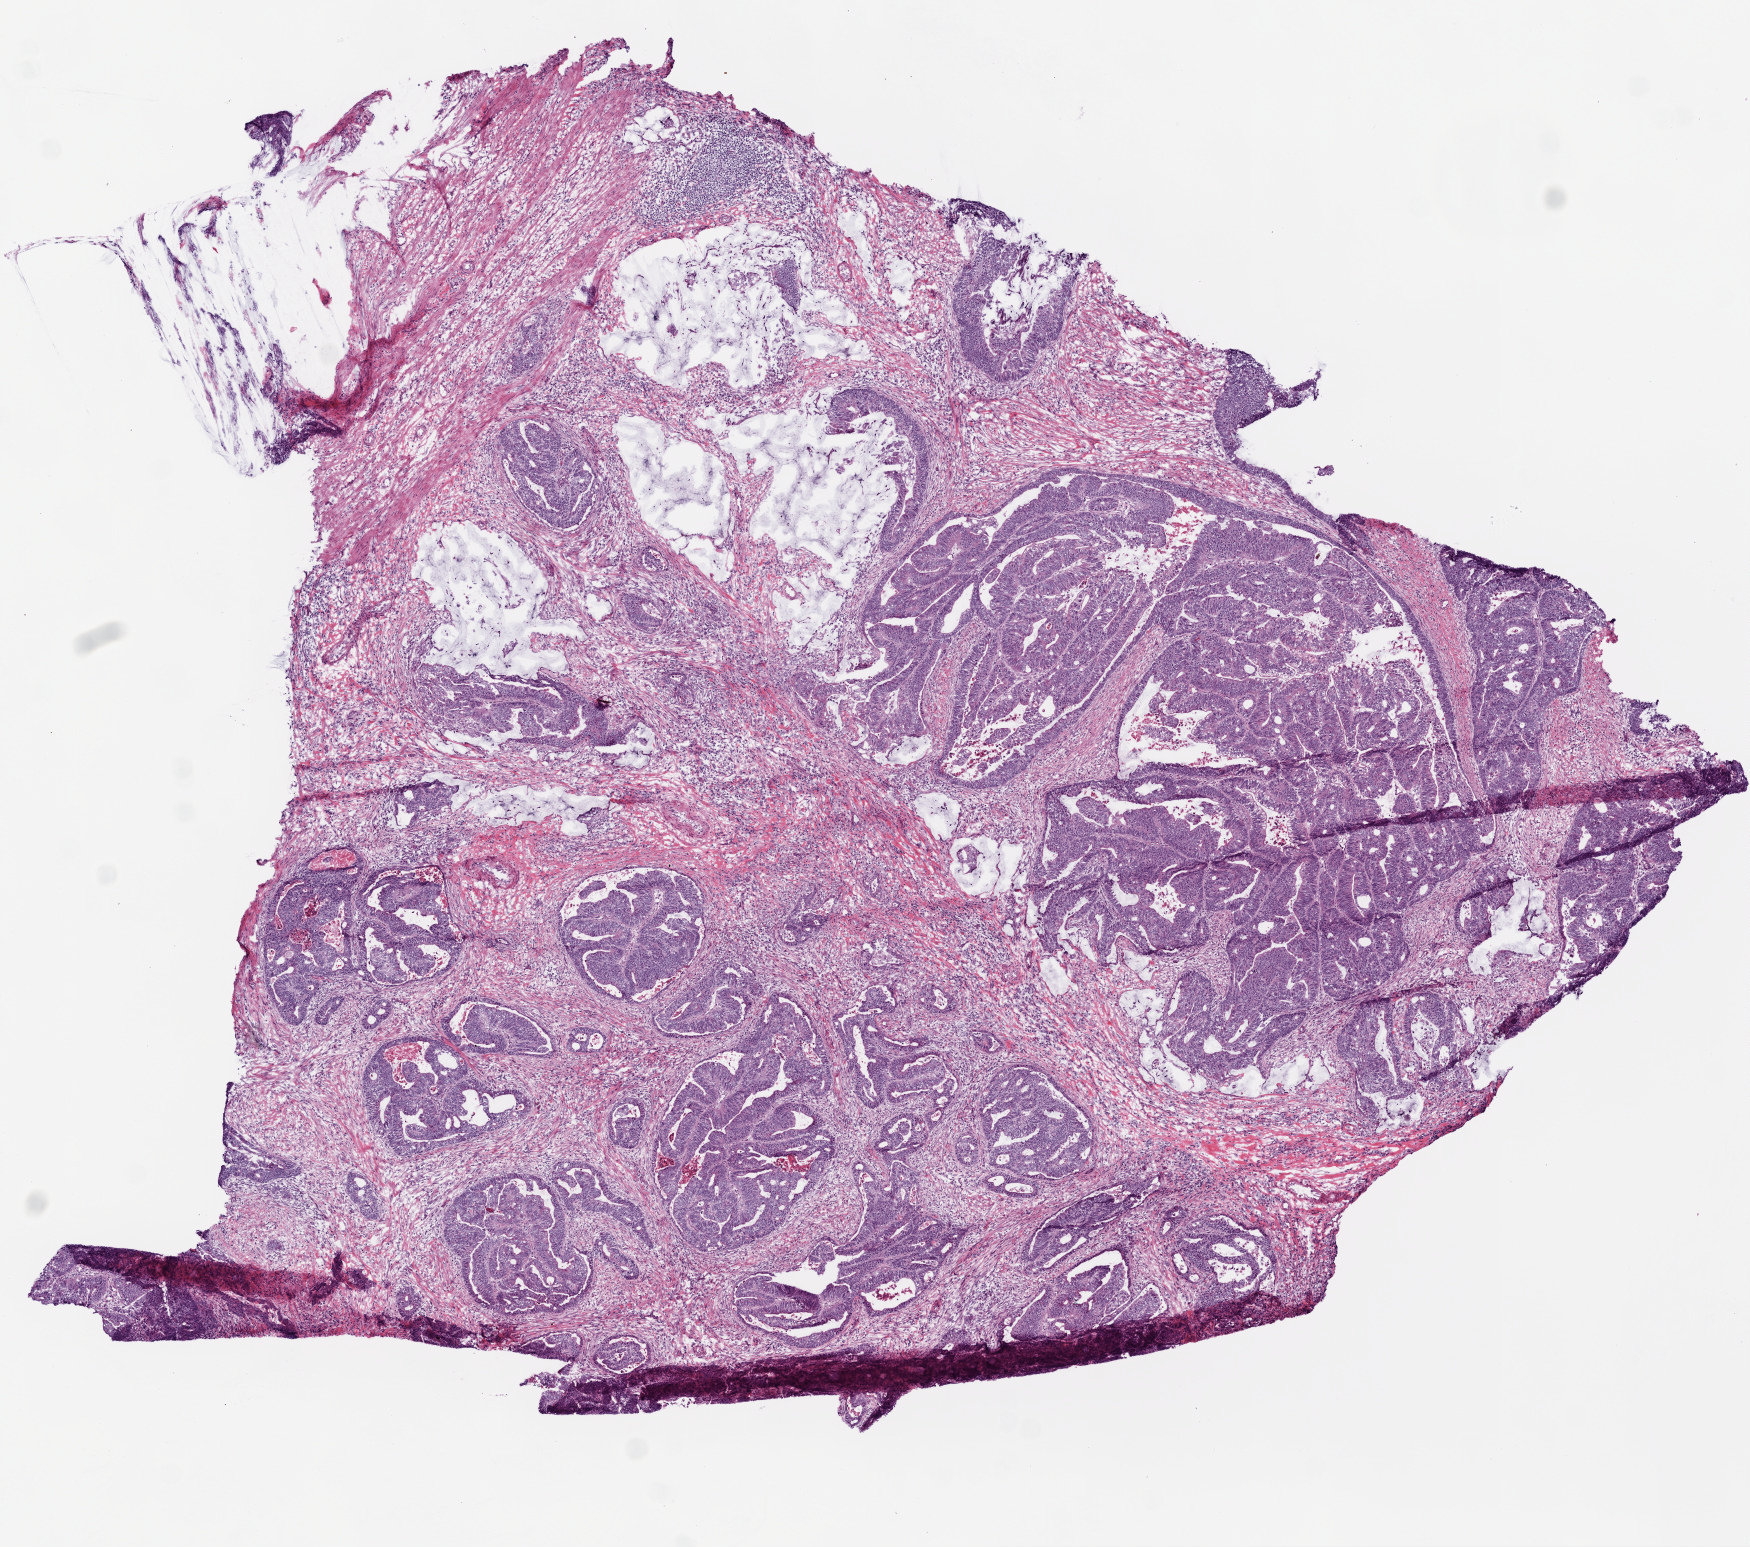
Digitized H&E-stained tissue section (whole slide) — a low-resolution overview of the entire scanned area, about 7.0 x 6.2 mm, frozen section, primary tumour sample from the colon. Female patient; age at initial diagnosis 53 years. Pathologist review of this section (percent, as recorded): tumour cells 25%, tumour nuclei 60%, normal cells 0%, stromal cells 70%, necrosis 5%.
* AJCC pathologic stage: II (5th edition)
* lymph nodes positive (case pathology): 0 of 41 examined
* diagnosis: Adenocarcinoma, NOS (transverse colon)